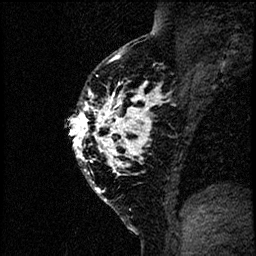
Breast MRI (dynamic contrast-enhanced), one sagittal slice. Position 42 of 60 along the scan axis. Dynamic contrast-enhanced study with each time point stored as its own series, time point 2 of 4 at this slice position (early post-contrast, ordered by acquisition time). 1.5 T. TE 4.2 ms, TR 17.6 ms. 256 × 256 image matrix, field of view 200 × 200 mm. Patient: female, 40 years. Case-level facts recorded for this patient, not image findings: setting: breast cancer imaged before/during neoadjuvant chemotherapy; receptor status: HER2-positive.
Outlined on this slice (semi-automatically segmented with operator editing):
- analysis volume of interest (the breast-tissue region the enhancement analysis was run in; not a lesion): bounding box (x1, y1, x2, y2) in pixels: (66, 55, 185, 206)
- tumour enhancement mask (voxels above the 100 % enhancement threshold inside the analysis volume of interest): (68, 56, 156, 168)